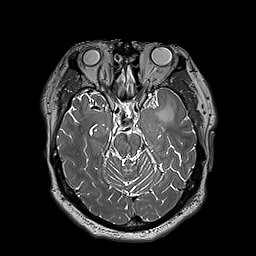
Brain MRI from a brain-tumour surgery series, one axial slice. Position 124 of 192 along the scan axis. 256 × 256 image matrix. From the clinical record (not read from this slice): histopathology: Astrocytoma; WHO grade: 3; IDH mutation: yes; tumour location: Left Insular.
Annotated regions visible in this slice (outlined manually by an expert reader):
- tumour: box from (x=155, y=105) to (x=174, y=123) px